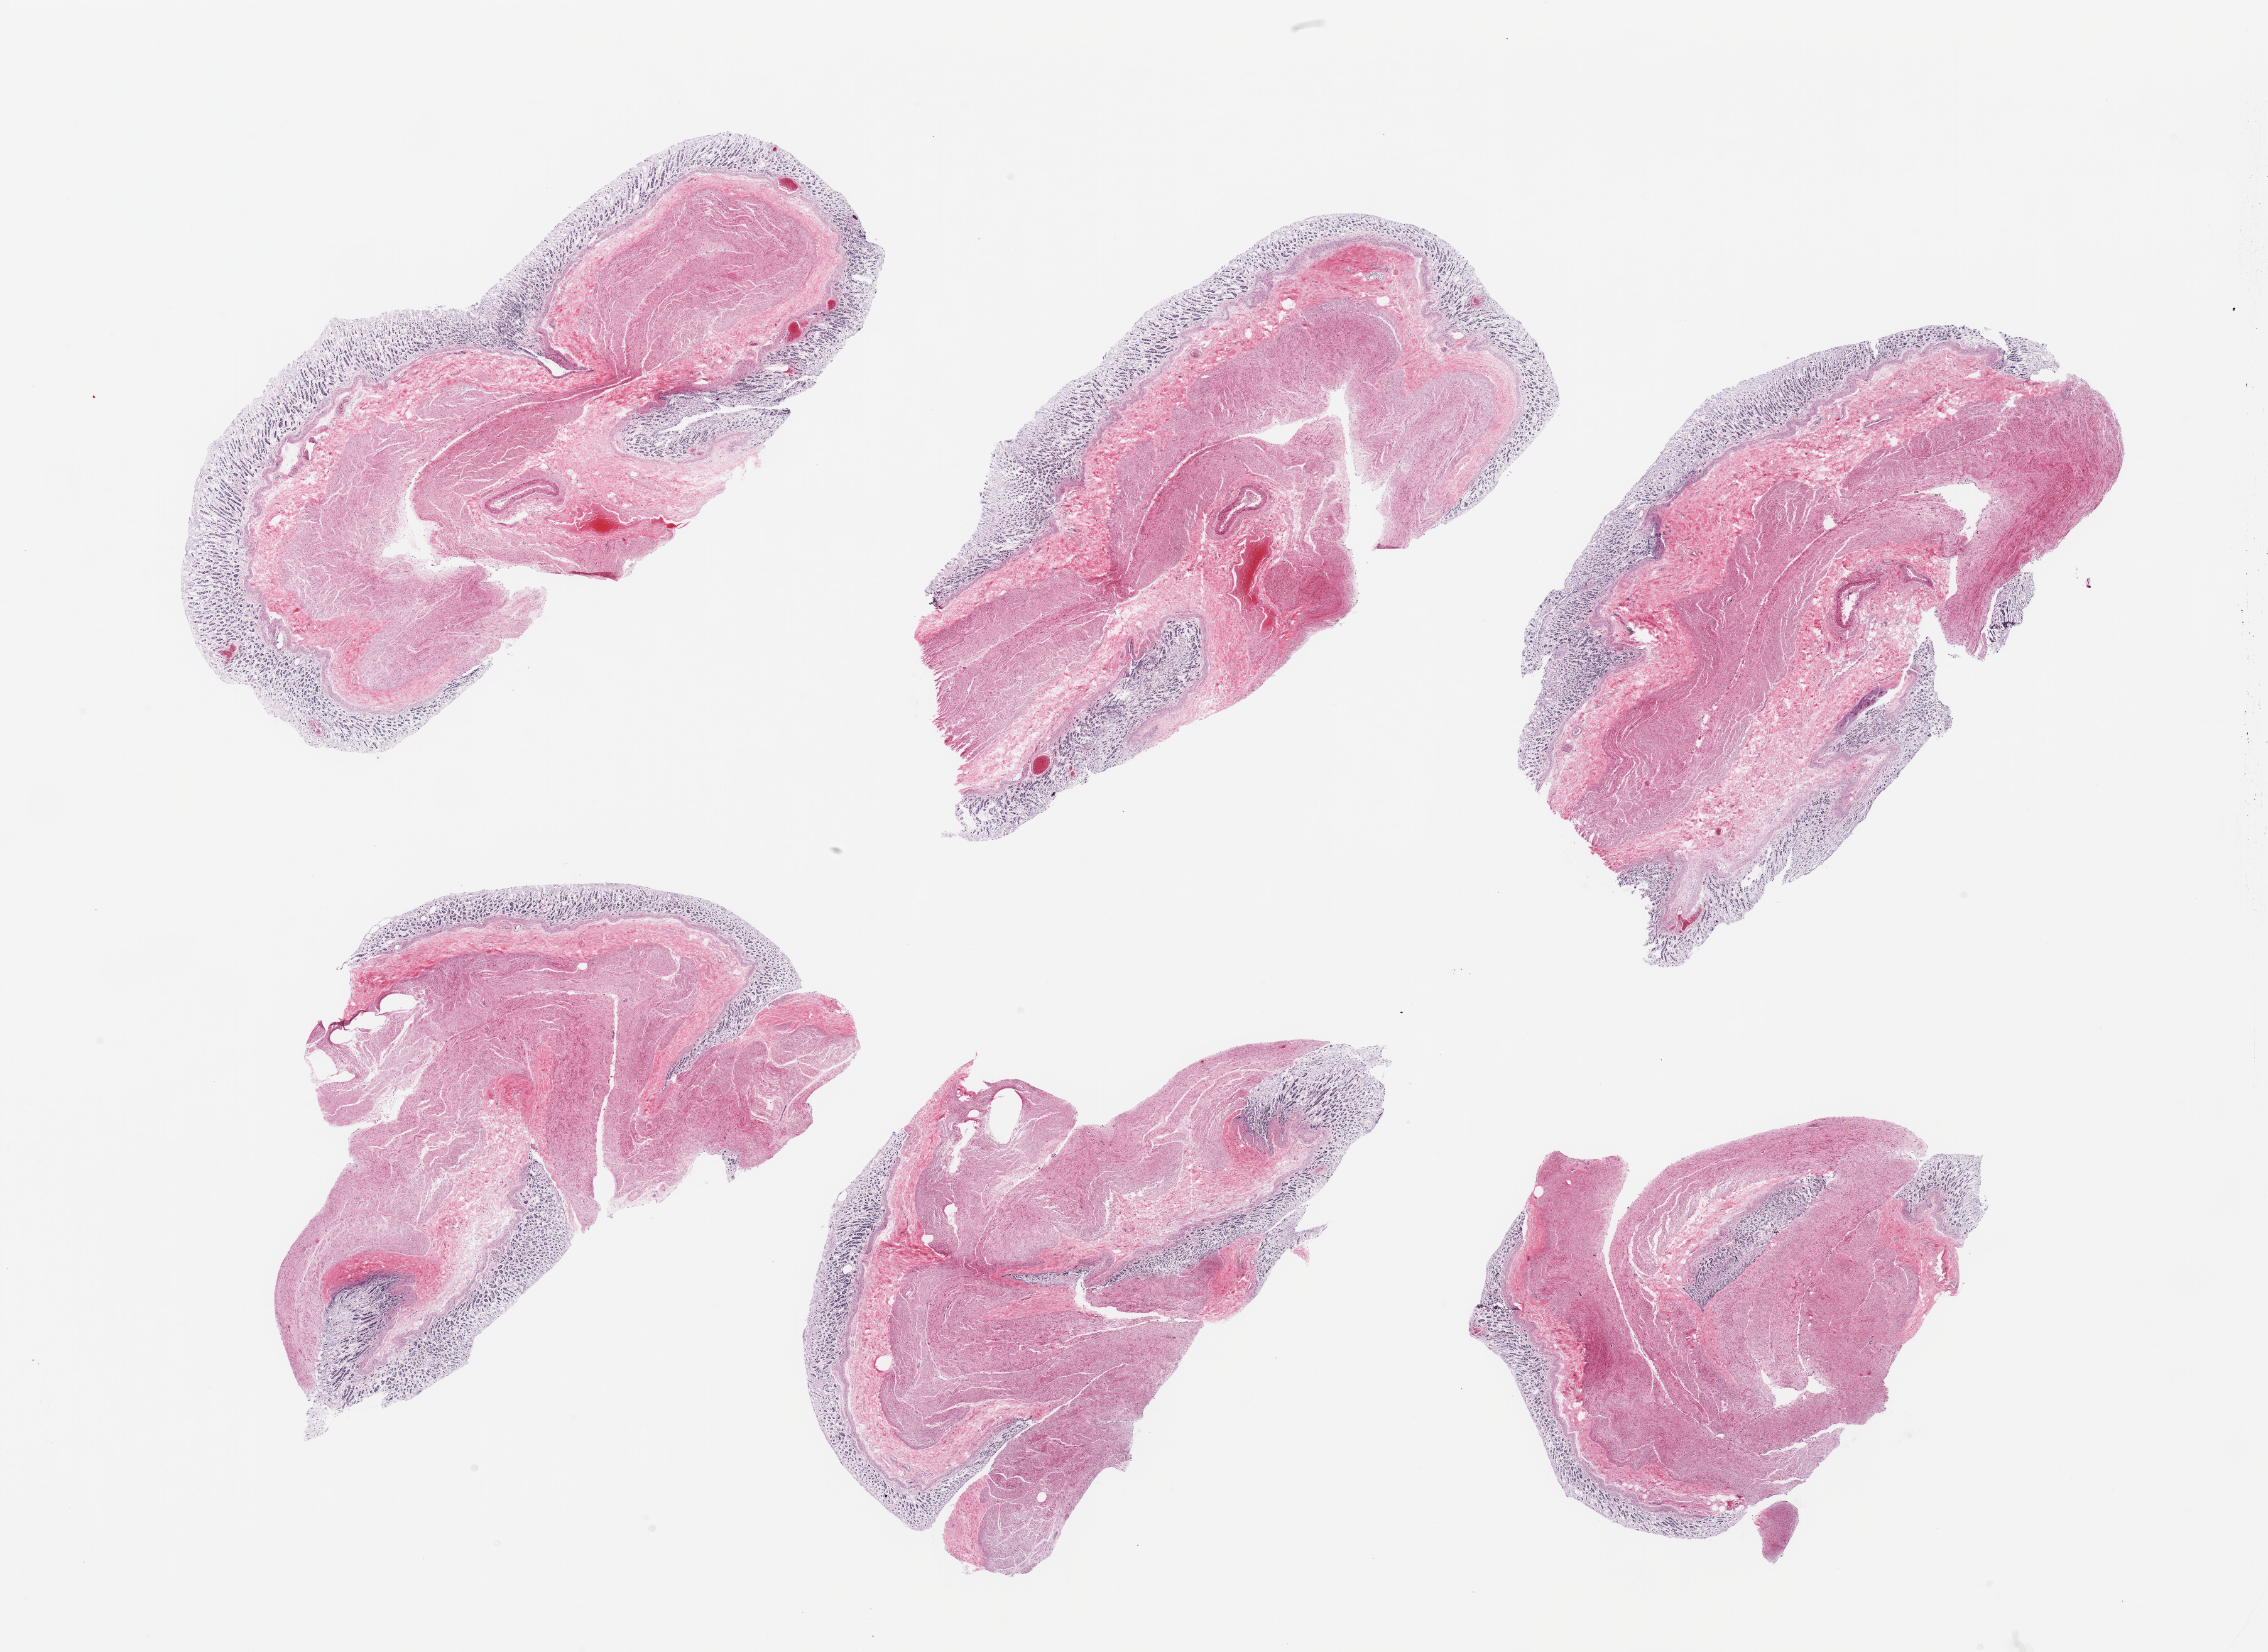
Whole-slide image, H&E stain — whole scanned area (about 28.5 x 20.8 mm) shown as a low-resolution overview; PAXgene-fixed paraffin-embedded (PFPE) section; target tissue: stomach; tissue donor sample. Donor: female.
Reviewer comment on this tissue sample: 6 pieces; full thickness sections, mucosa and muscularis are largely autolyzed.